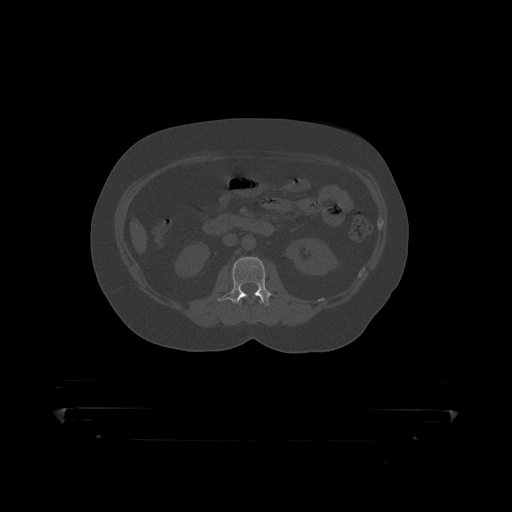
CT including the spine, one axial slice; position 122 of 390 along the scan axis; reconstruction kernel STANDARD; 120 kVp; bone window (W 1800 / L 400 HU); 1.25 mm slice thickness; 512 × 512 image matrix, field of view 650 × 650 mm. Patient: male, 60 years. From the clinical record (not read from this slice): primary cancer: prostate.
Structures marked on this image (semi-automatically segmented with operator editing):
- L1 vertebra: bounding box [x1, y1, x2, y2] px = [240, 300, 263, 306]
- L2 vertebra: [218, 257, 272, 307]